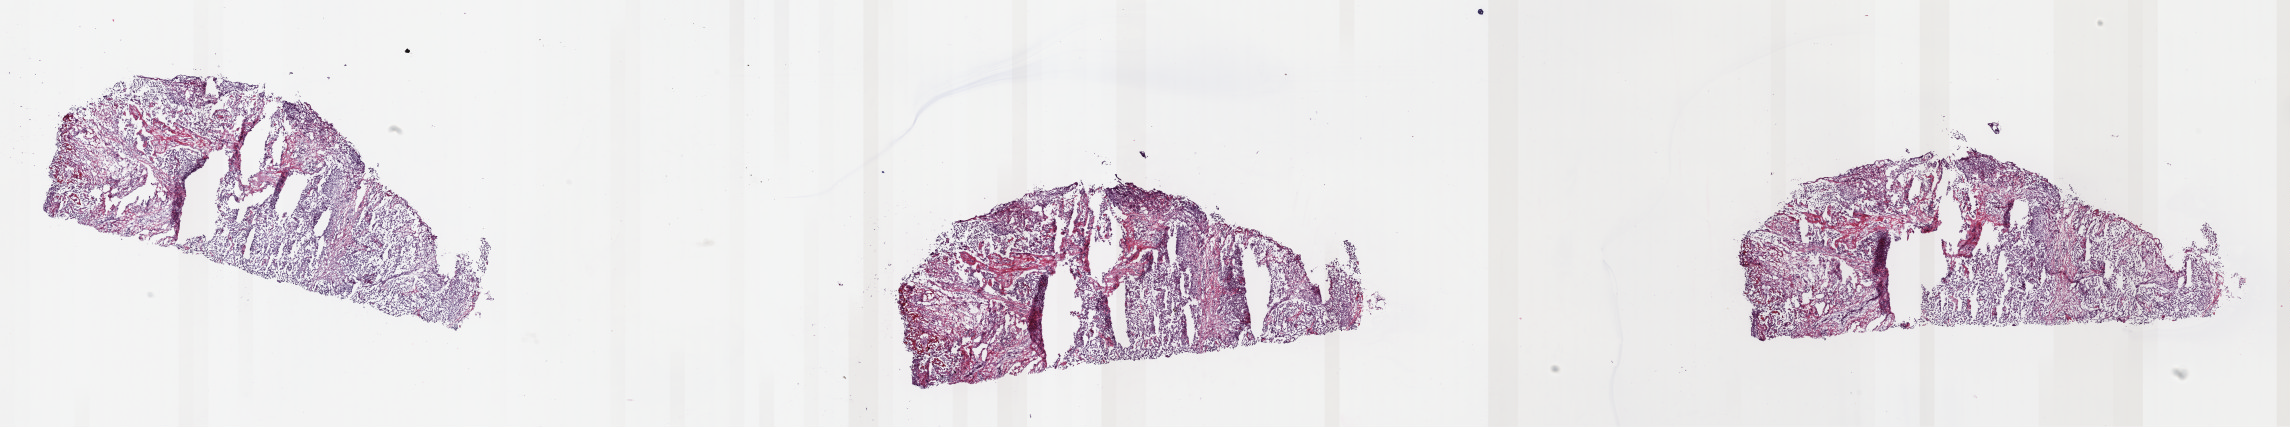
Whole-slide histology image, H&E — a low-resolution overview of the entire scanned area, about 36.0 x 6.7 mm (slide scanned at 40x); frozen section; mesothelium, primary tumour sample. Male patient; age at initial diagnosis 60 years. Slide review estimates, as recorded: tumour cells 100%, tumour nuclei 88%, normal cells 0%, stromal cells 0%, necrosis 0%. Inflammatory infiltration, as recorded: lymphocyte infiltration 0%, monocyte infiltration 0%, neutrophil infiltration 0%.
Pathologic diagnosis: Mesothelioma, malignant (pleura, NOS). AJCC pathologic stage: IV (6th edition).